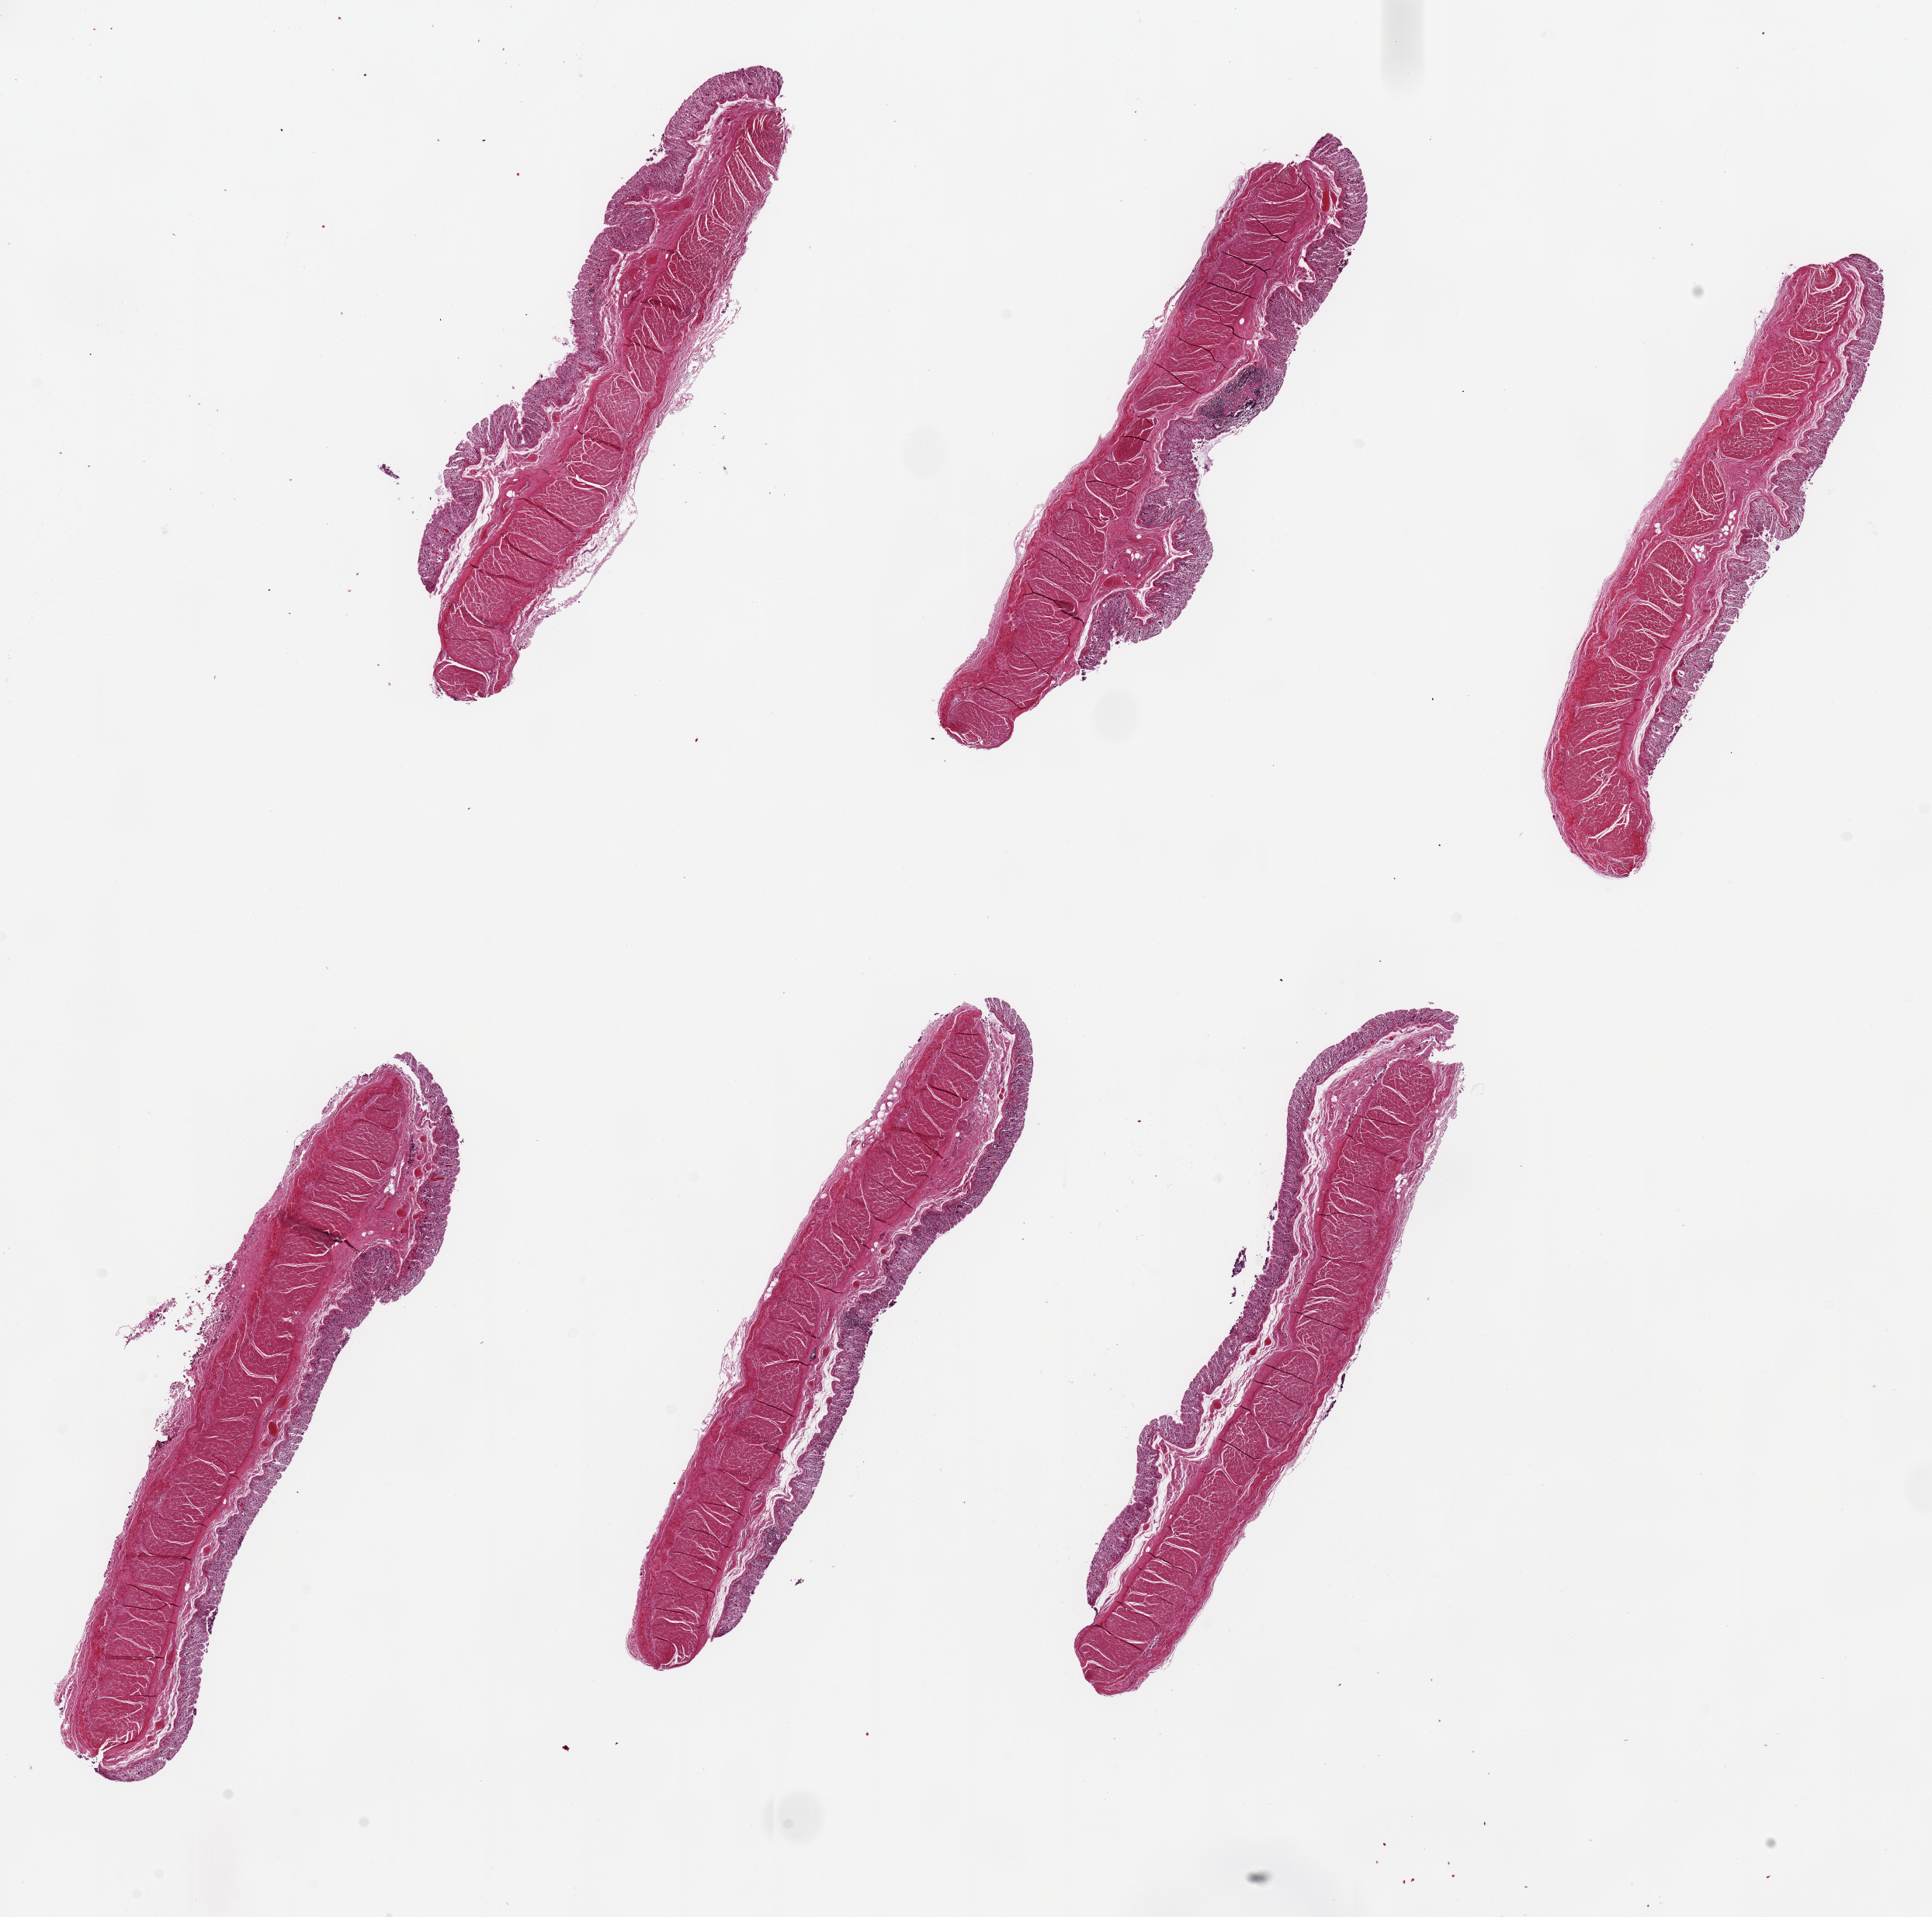
Digitized hematoxylin and eosin (H&E)-stained section — whole scanned area (about 19.7 x 19.5 mm) shown as a low-resolution overview. PAXgene-fixed paraffin-embedded (PFPE) section. Sampled site (target tissue): transverse colon. Tissue donor sample. Donor sex: male.
Reviewer comment on this tissue sample: 6 pieces, up to 8x3mm; ~10% thickness is mucosa but badly autolyzed.